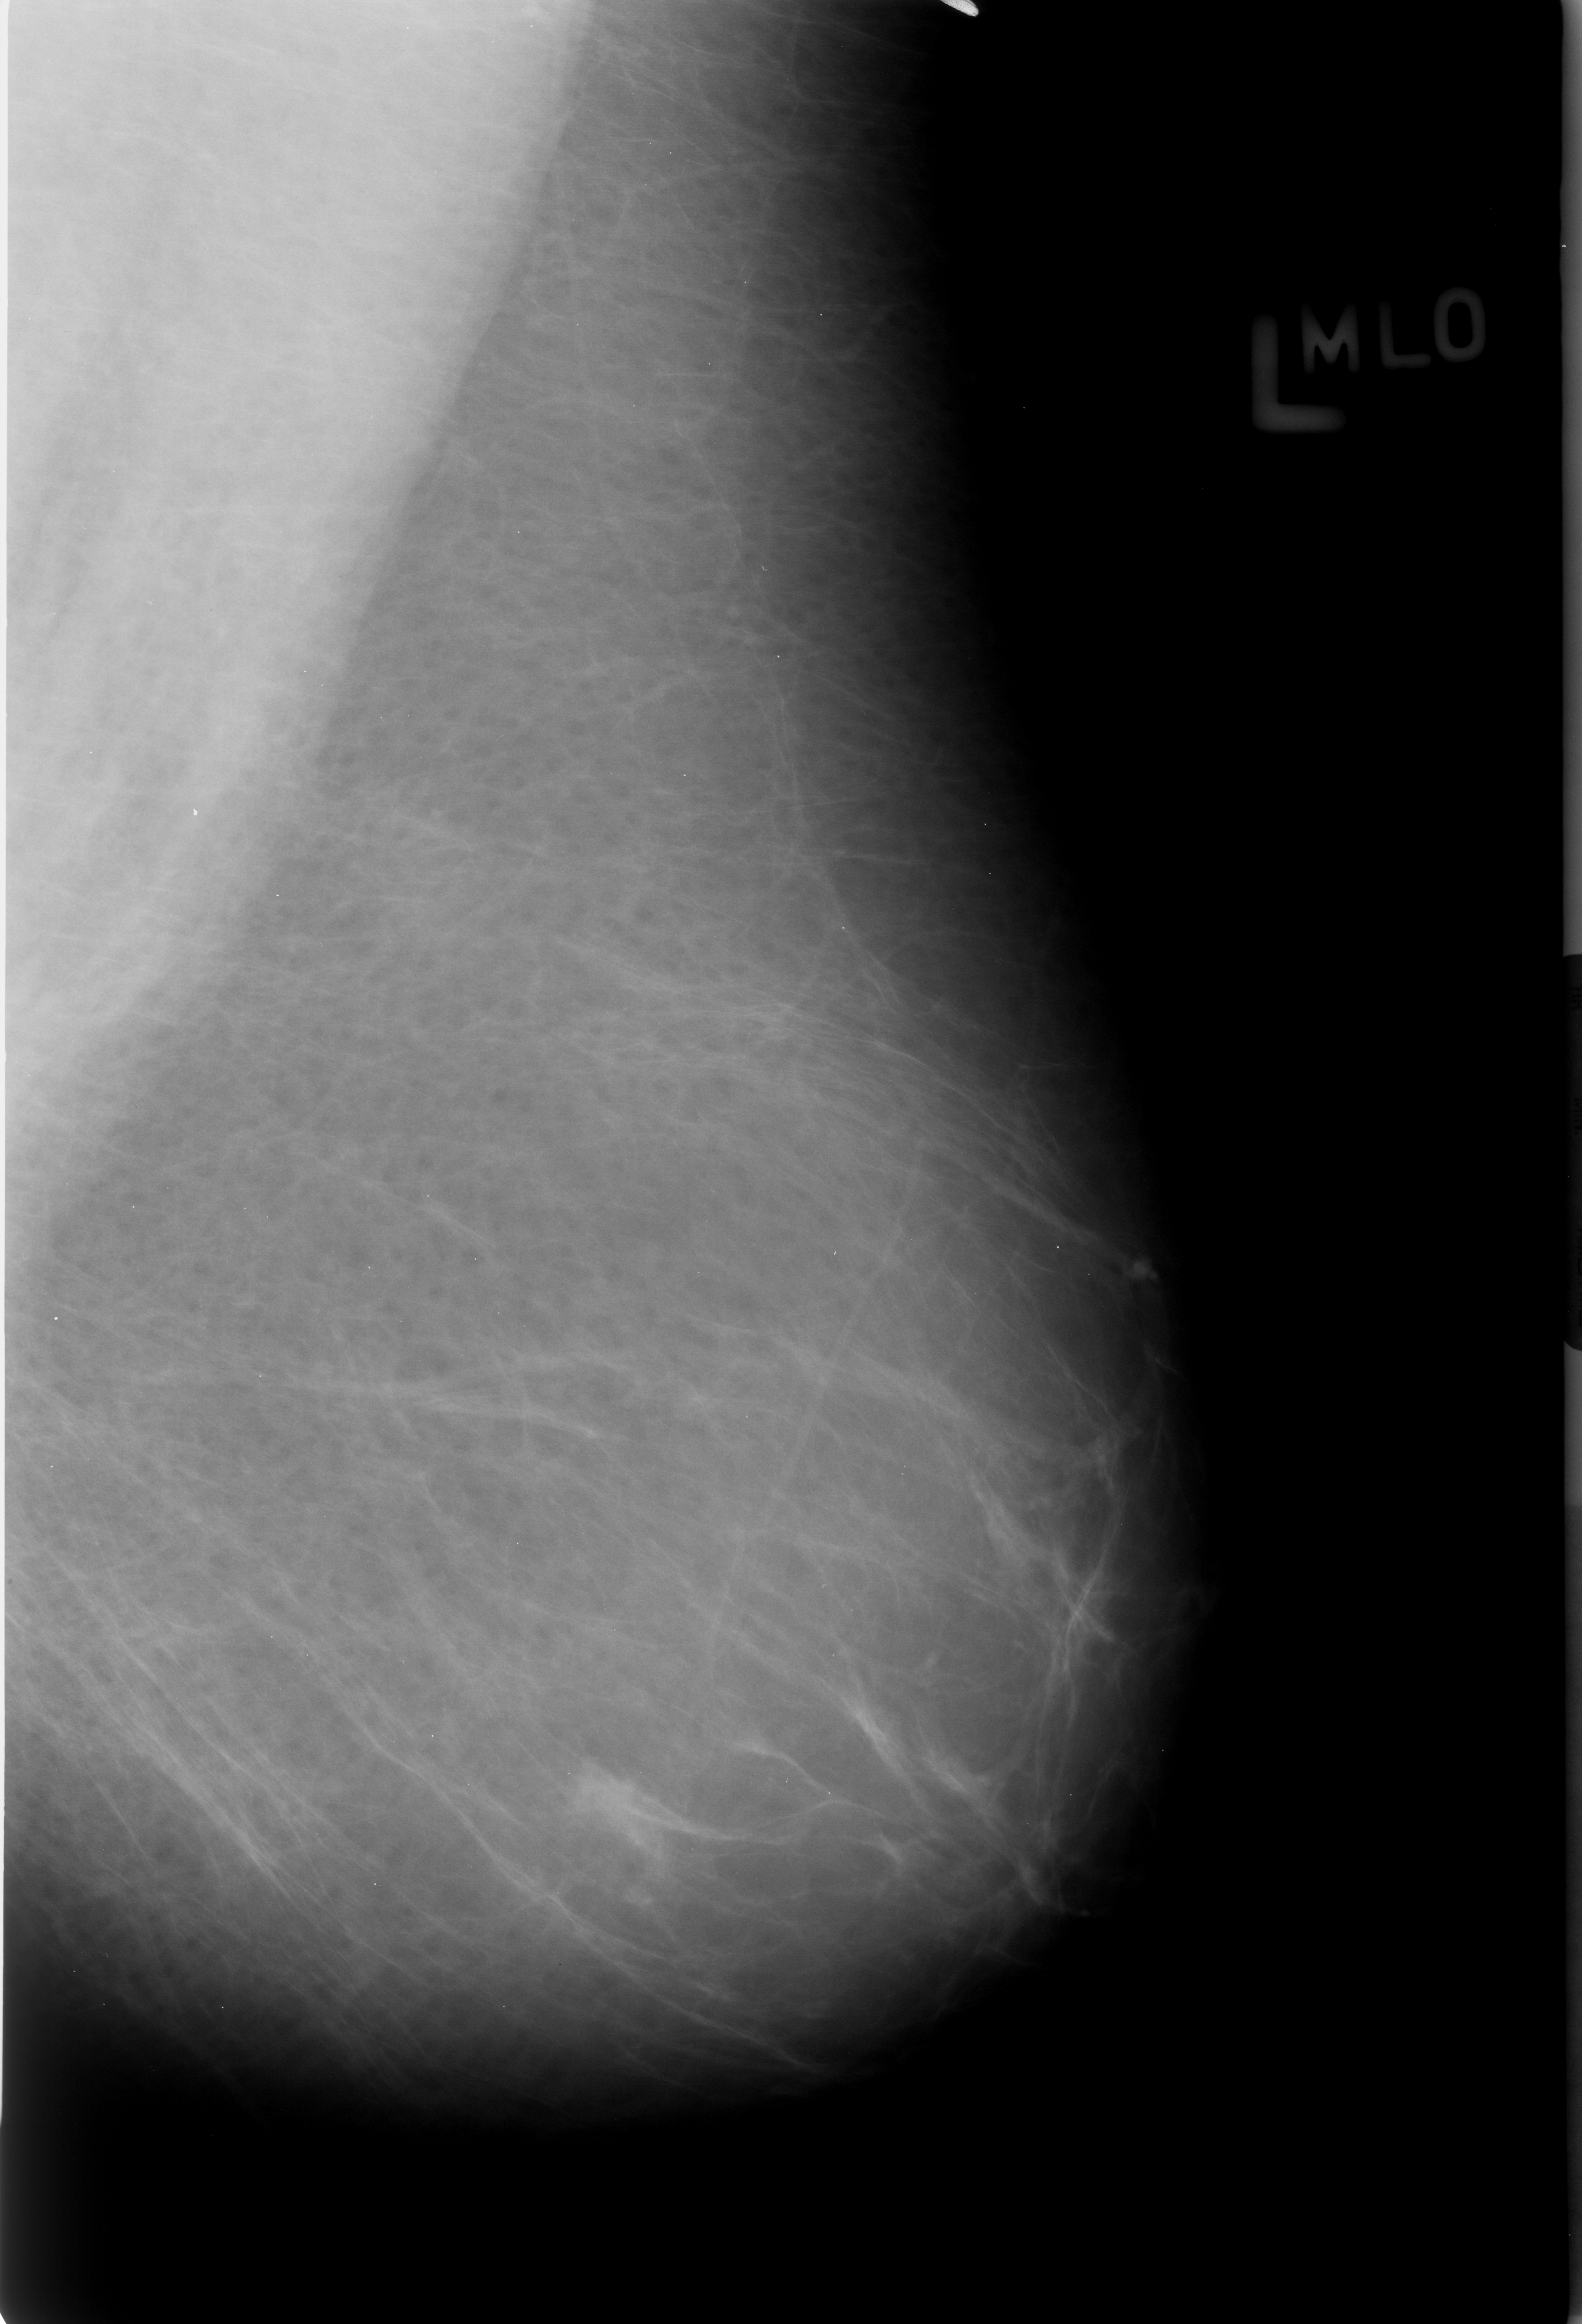
Scanned film-screen mammogram. Left breast. Mediolateral oblique (MLO) view. Breast composition: almost entirely fatty (BI-RADS density category 1 of 4). 1582 × 2324 image matrix.
Expert-marked regions of interest on this film, with their recorded descriptors:
- mass, shape irregular, margins ill defined; BI-RADS assessment category 4; pathology result (as recorded, not read from the image): benign: bounding box <564,1761,692,1876> (left, top, right, bottom; pixels)